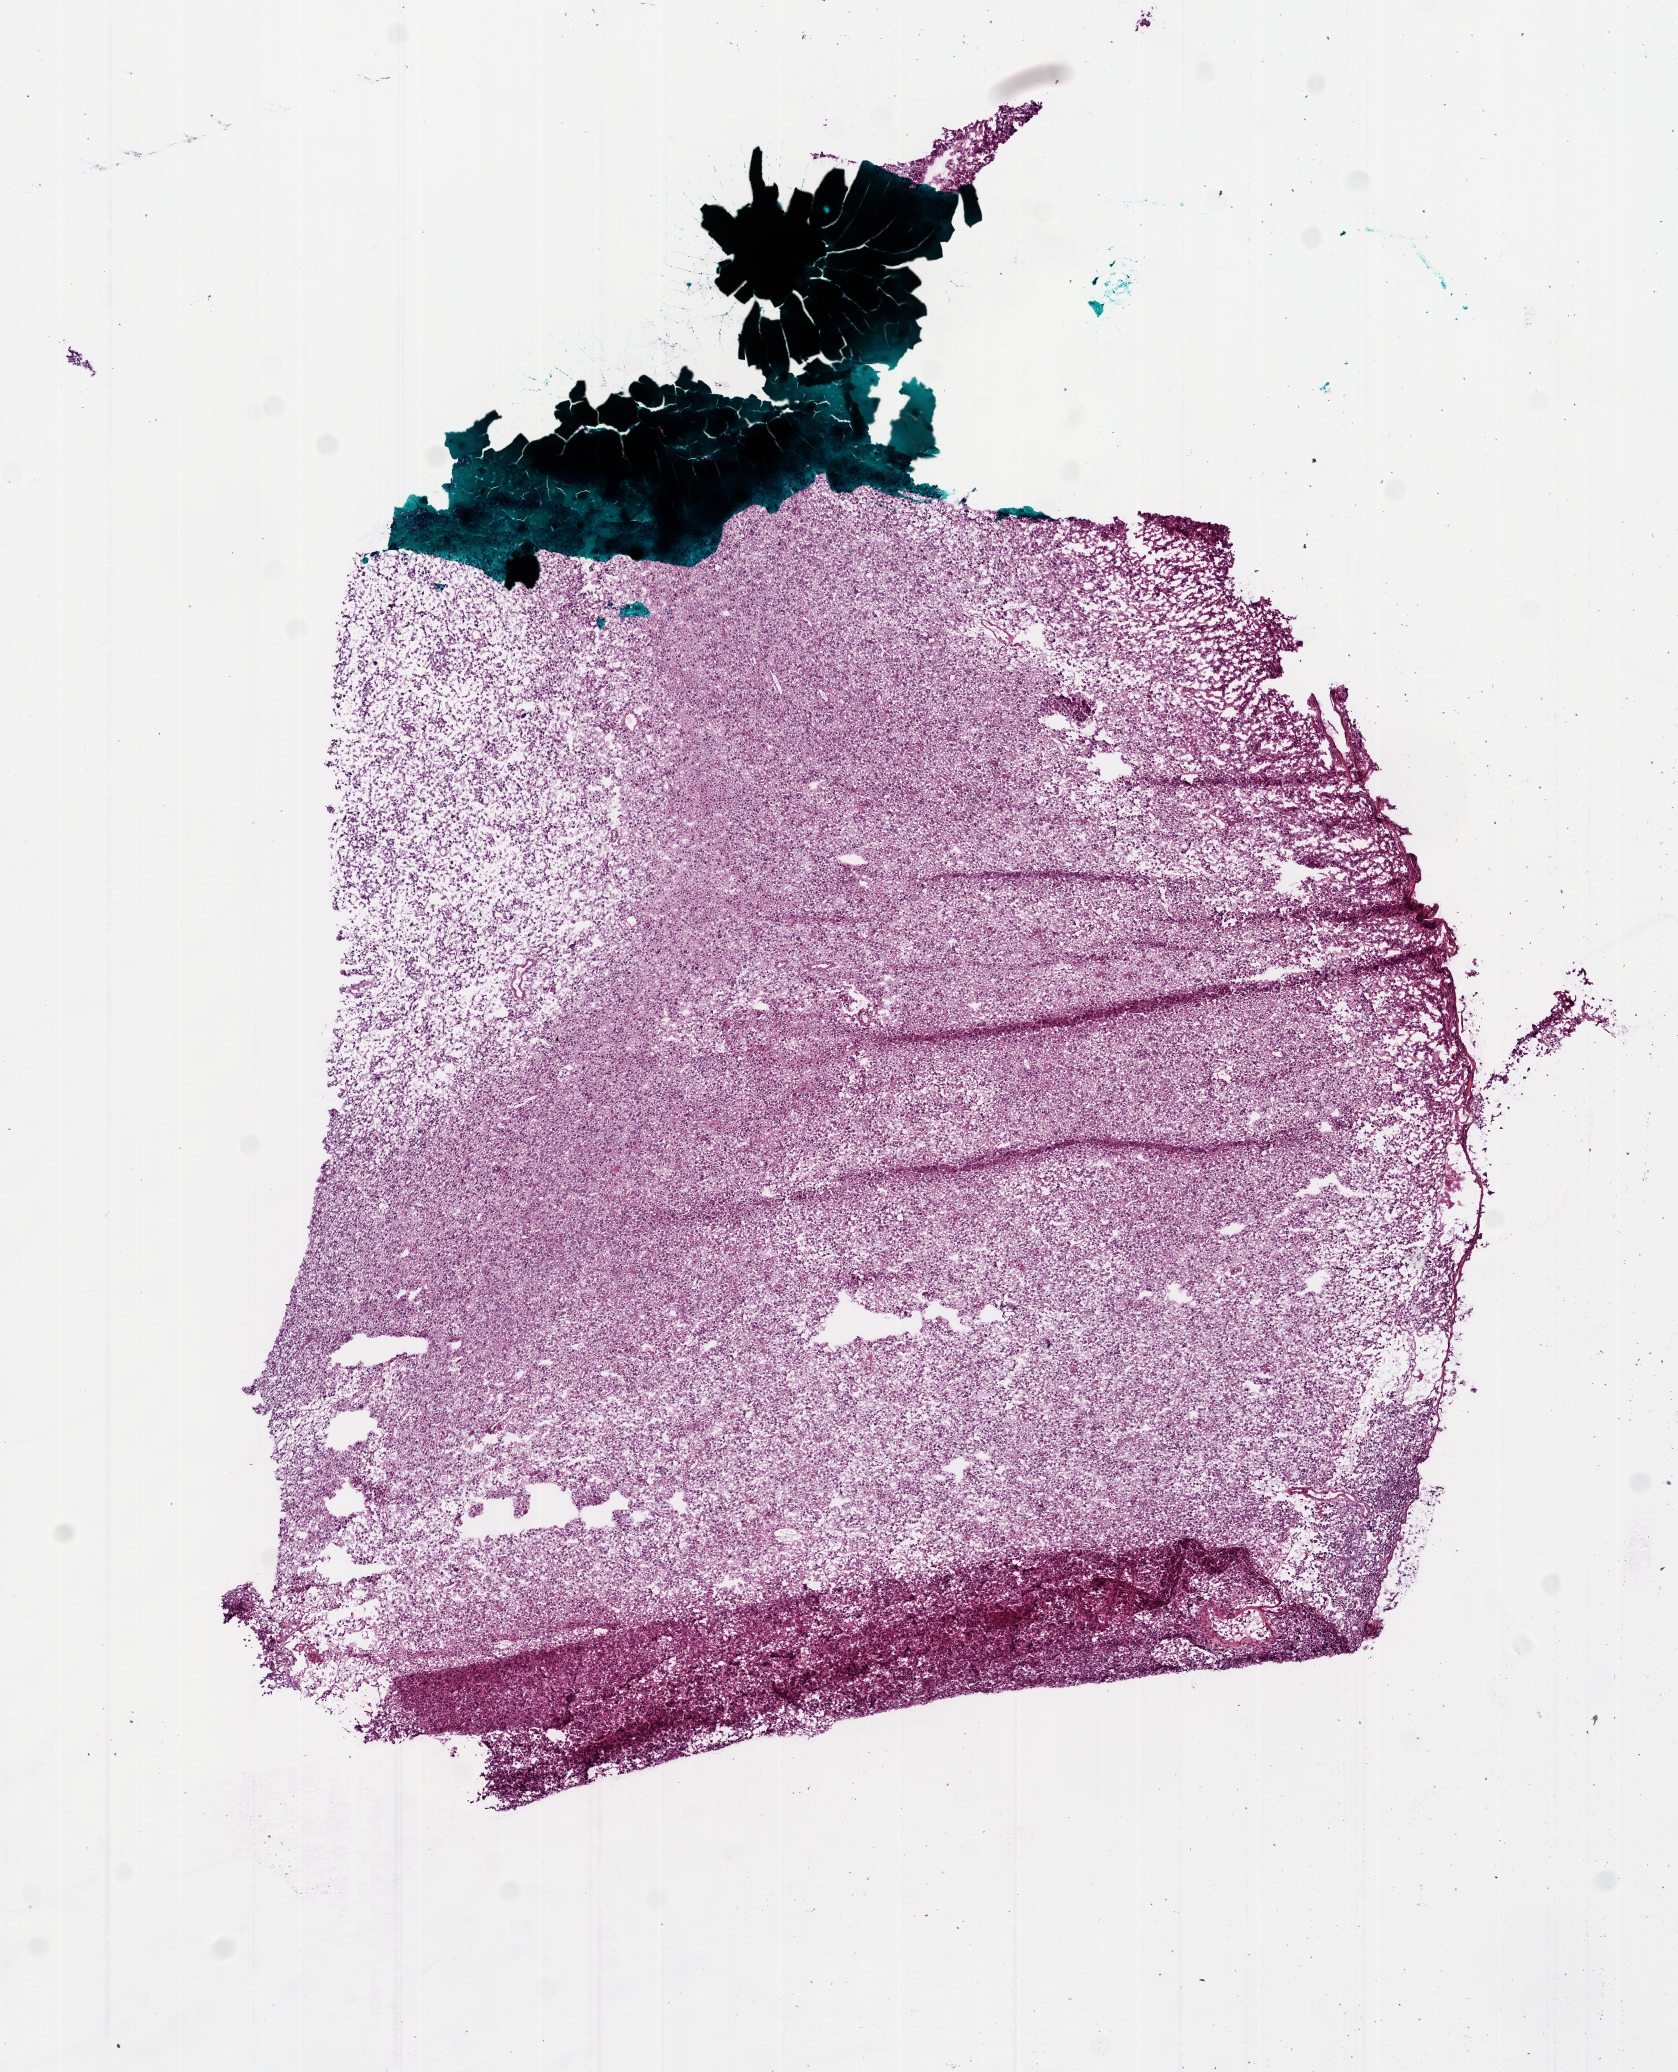
Whole-slide histology image, Hematoxylin and eosin (H&E) stained, whole scanned area (about 6.8 x 8.4 mm, slide scanned at 20x) shown as a low-resolution overview; frozen section from the bottom of the tissue portion; sample: primary tumour, brain. Male patient; age at initial diagnosis 17 years. Slide review estimates, as recorded: tumour cells 75%, tumour nuclei 90%, normal cells 0%, stromal cells 10%, necrosis 15%.
Pathologic diagnosis: Glioblastoma.